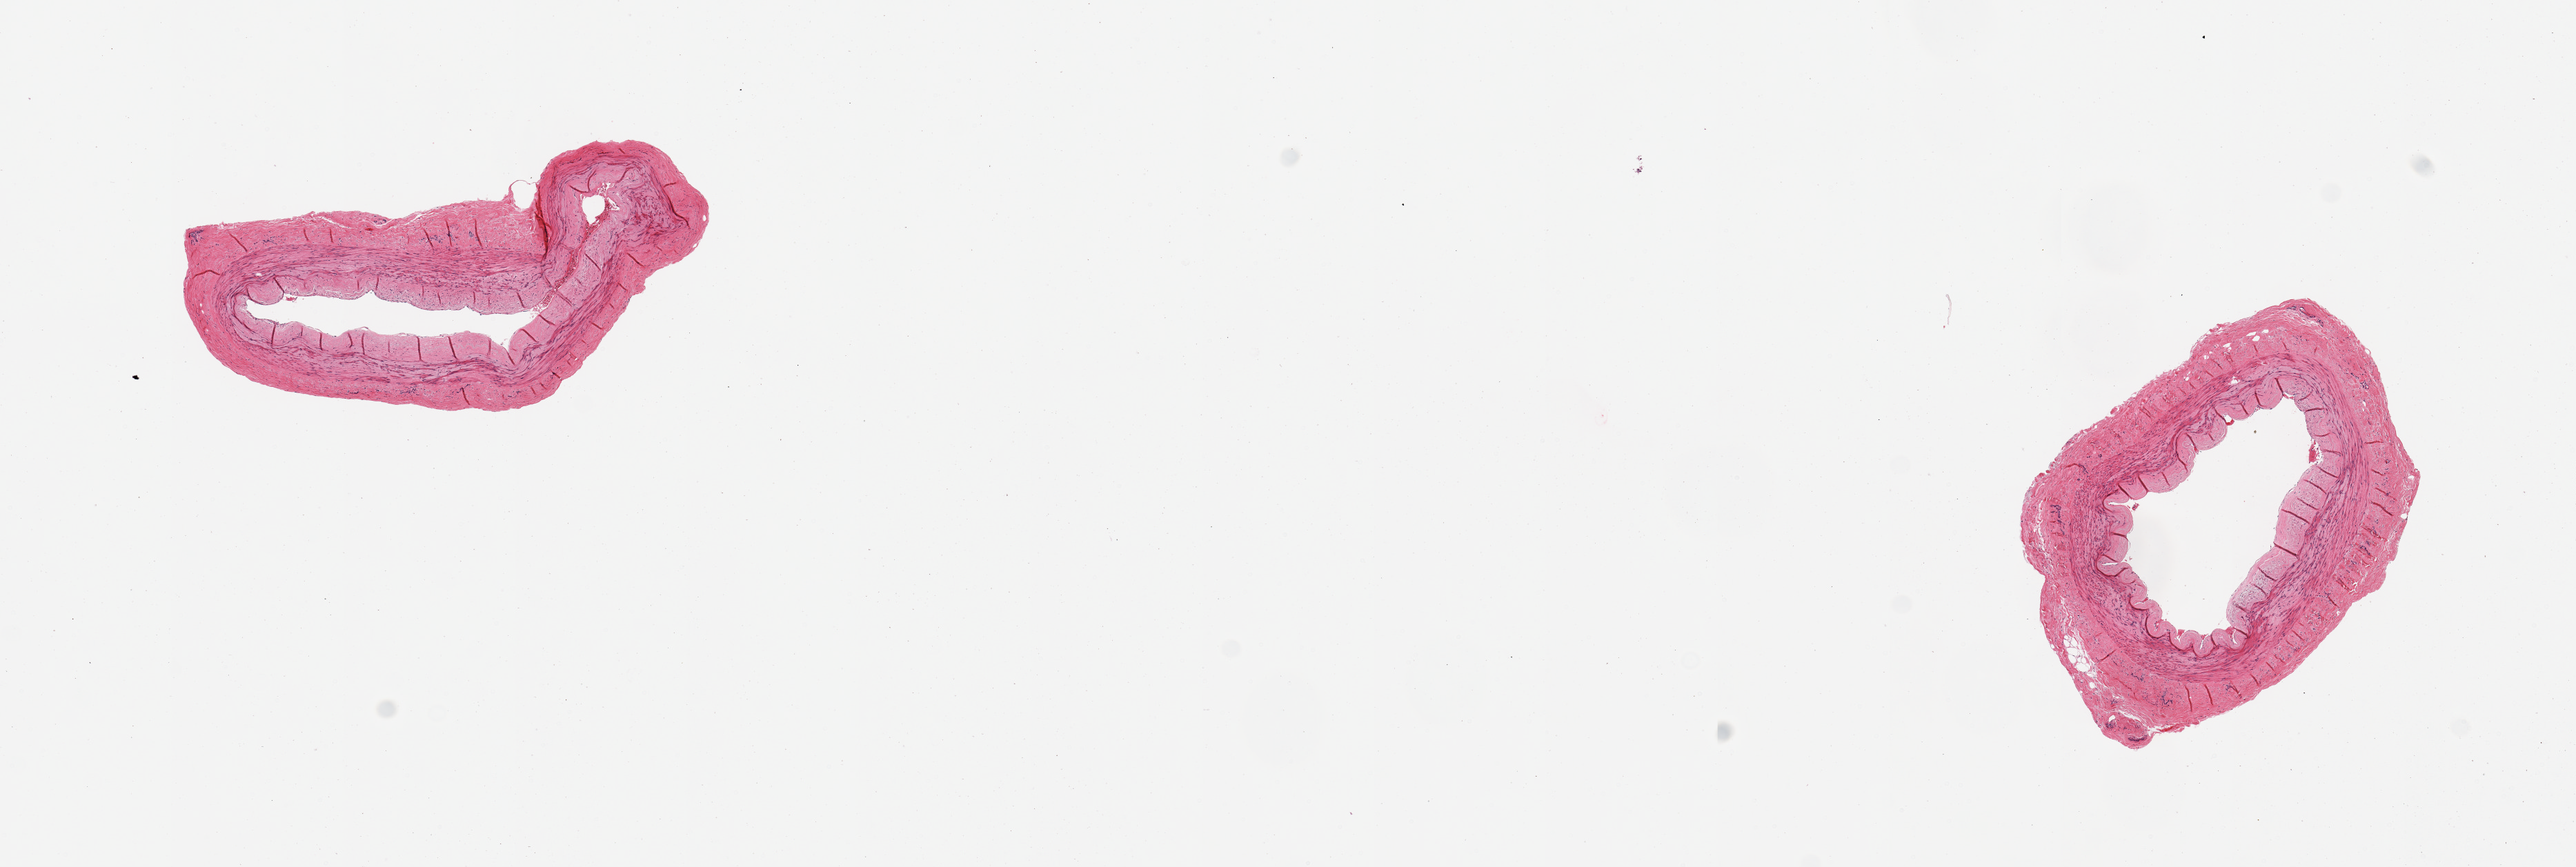
Hematoxylin and eosin (H&E) whole-slide image, brightfield, a low-resolution overview of the entire scanned area, about 14.8 x 5.0 mm (acquisition: 20x scan), PAXgene-fixed, paraffin-embedded tissue, section of tibial artery (target tissue), tissue donor sample. Male donor.
Reviewer comment on this tissue sample: 2 pieces, clean specimens; no significant atherosis.